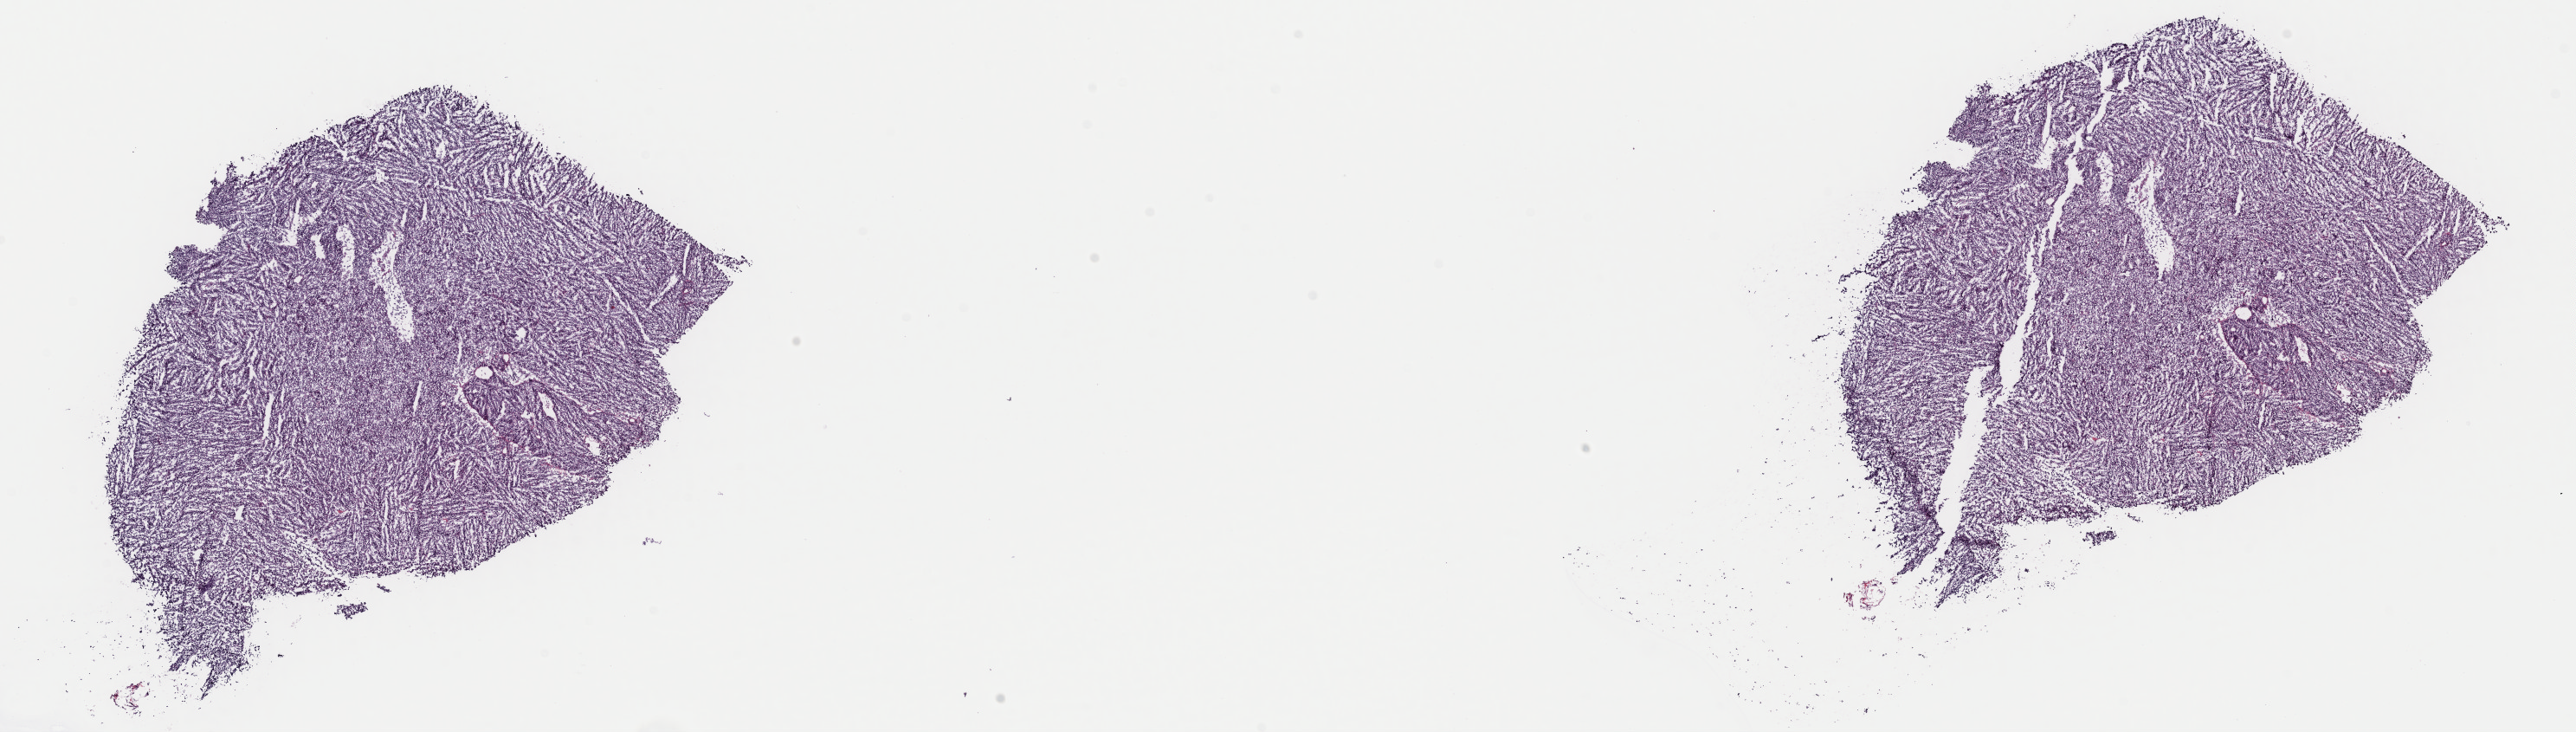
Whole-slide histology image, Hematoxylin and eosin (H&E) stained — whole scanned area (about 23.5 x 6.7 mm) shown as a low-resolution overview; frozen section from the top of the tissue portion; lymphoid tissue, primary tumour sample. Female patient; age at initial diagnosis 58 years. Composition of this section per pathologist review: tumour cells 90%, tumour nuclei 90%.
Pathologic diagnosis: Diffuse large B-cell lymphoma, NOS (lymph nodes of head, face and neck).